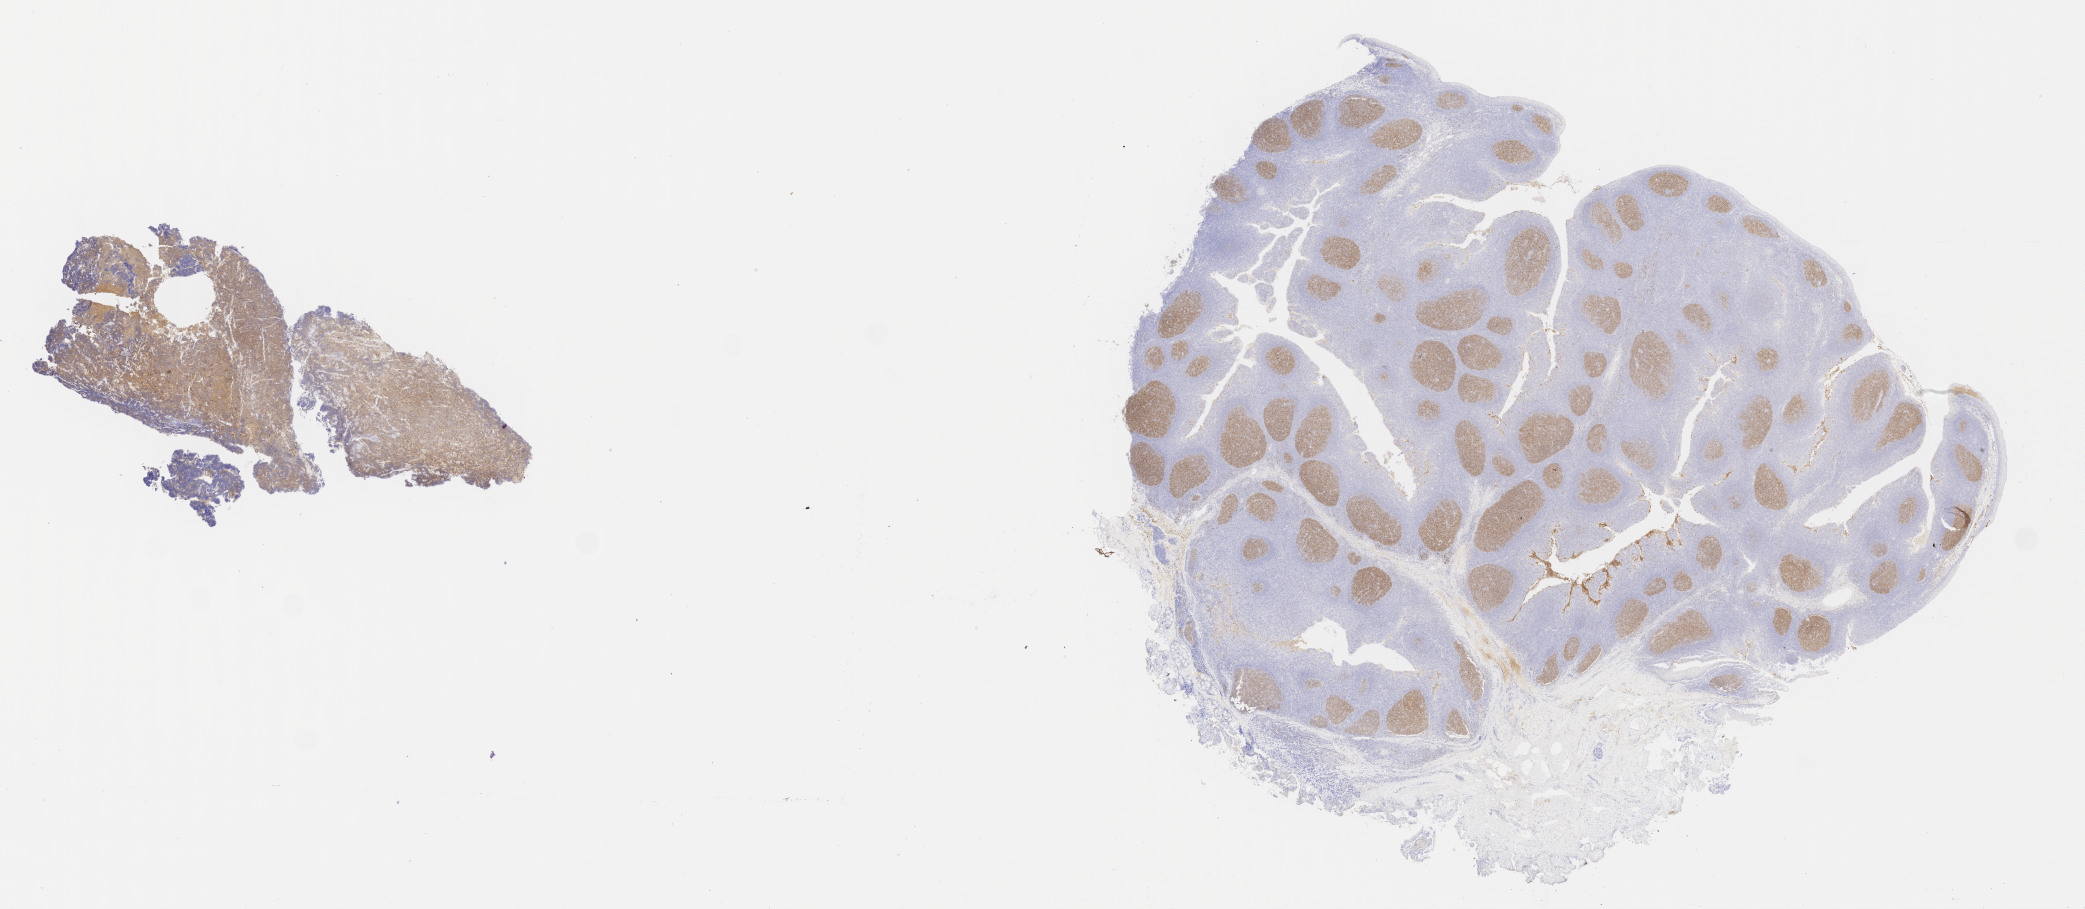
Whole-slide image, immunohistochemical stain for CD10 — low-resolution overview of the scanned area, about 33.7 x 14.7 mm; specimen: tumor tissue; site: mandible. Male patient, 25 years old.
Diagnosis: Diffuse large B-cell lymphoma, NOS.